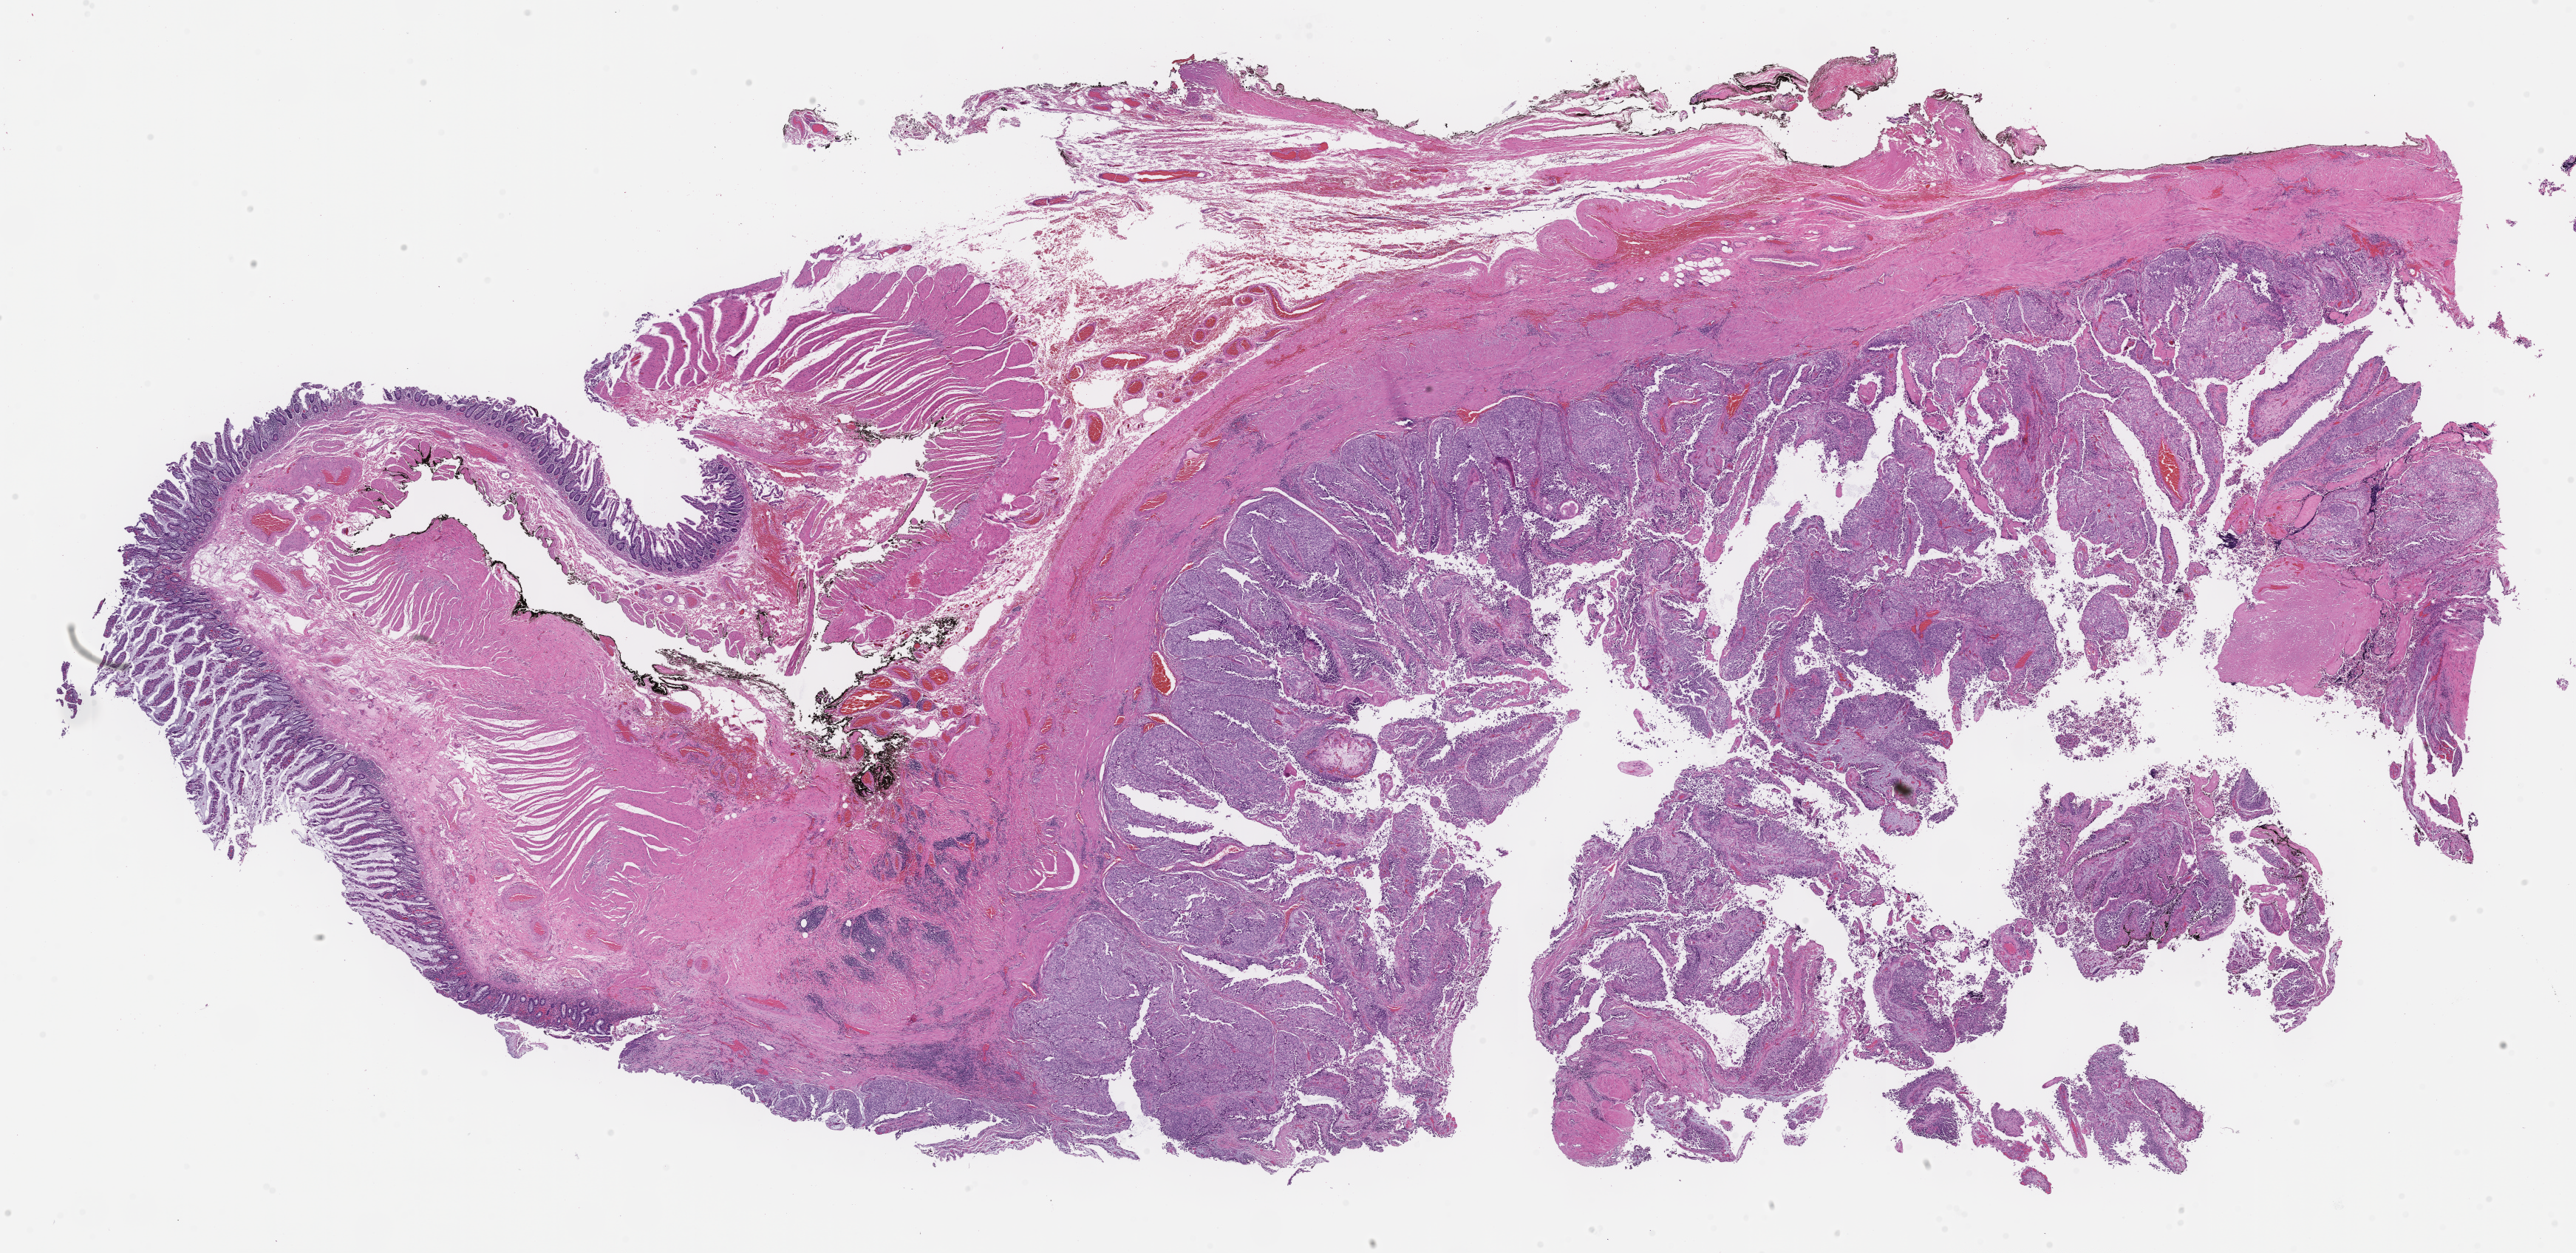
Haematoxylin and eosin whole-slide image, a low-resolution overview of the entire scanned area, about 28.1 x 13.7 mm. Formalin-fixed paraffin-embedded section. Recurrent tumor. Male patient. Pathologist review of this section (percent, as recorded): tumor cells 75%, tumor nuclei 75%, stromal cells 17%, necrosis 0%, normal cells 8%. Inflammatory infiltration, as recorded: lymphocyte infiltration 6%, monocyte infiltration 2%, neutrophil infiltration 4%.
• patient diagnosis: Carcinoma, metastatic, NOS
• section: bottom of the tissue portion